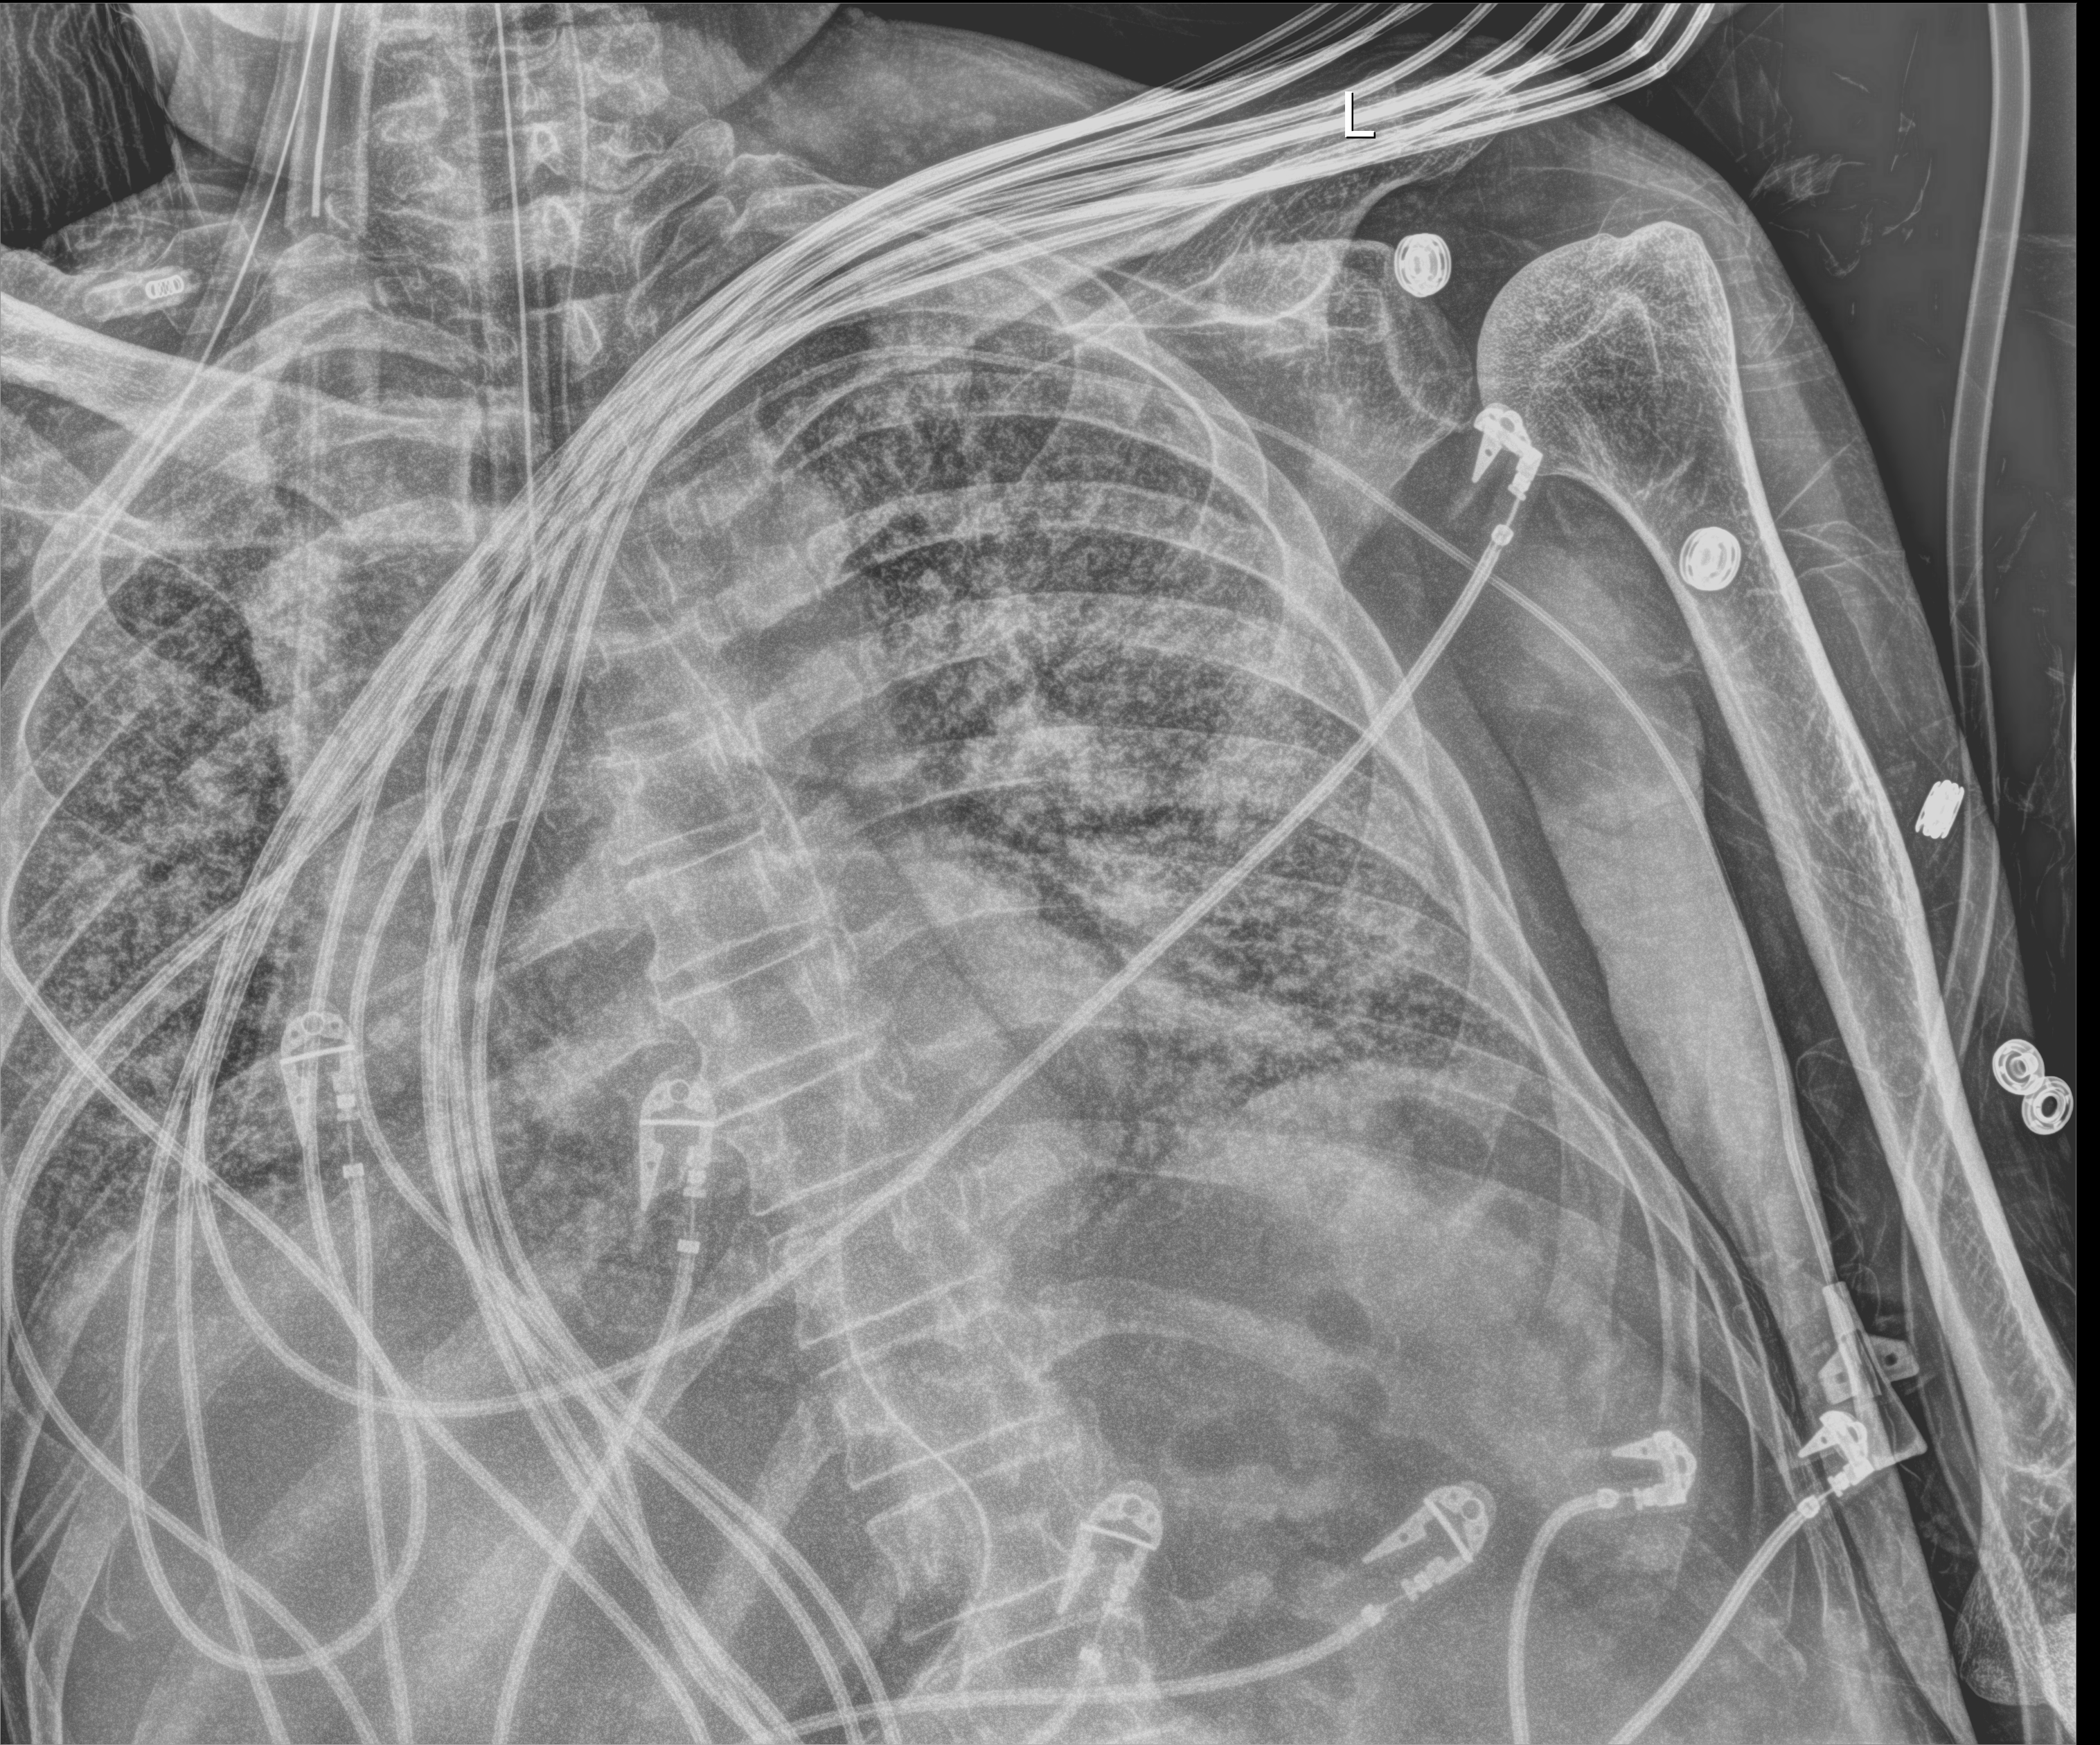
Chest X-ray, anteroposterior (AP) projection. Male patient hospitalised with COVID-19, age 60–74 years.
Hospital-stay facts (about this admission, not read from this image; timing relative to this image not recorded):
- mechanically ventilated during this hospital stay: yes